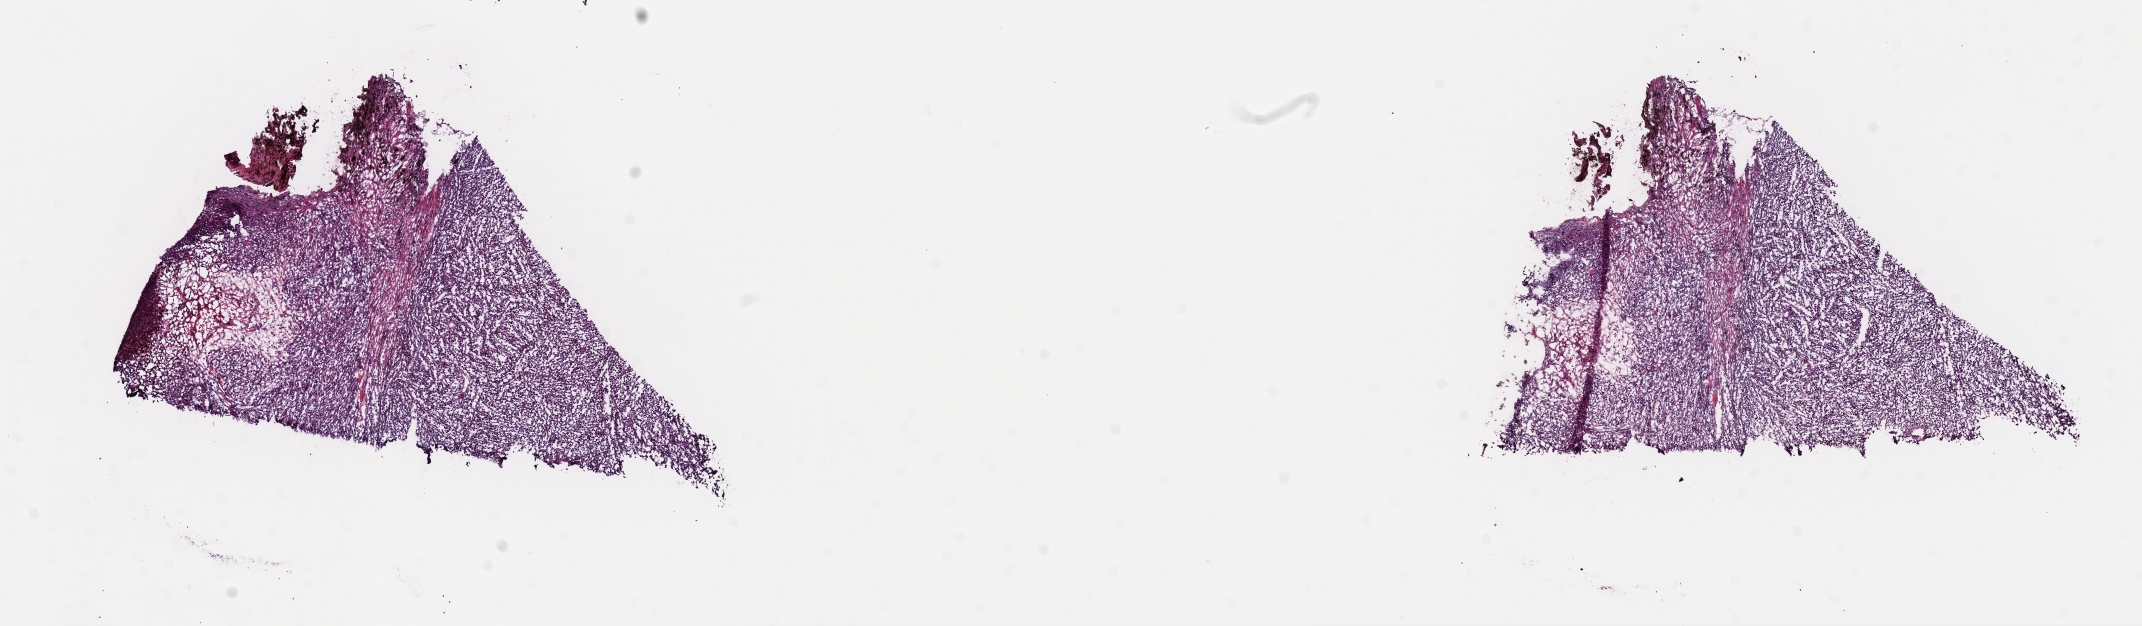
H&E whole-slide image, whole scanned area (about 16.9 x 4.9 mm, acquisition: 40x scan) shown as a low-resolution overview, frozen section from the top of the tissue portion, metastatic tumour sample, sampled site: connective, subcutaneous and other soft tissues of upper limb and shoulder. Male, age 71 years at initial diagnosis. Slide review estimates, as recorded: tumour cells 80%, tumour nuclei 80%, normal cells 0%, stromal cells 15%, necrosis 5%. Inflammatory infiltration, as recorded: lymphocyte infiltration 2%, monocyte infiltration 1%, neutrophil infiltration 0%.
This section: metastatic tumour tissue. Patient diagnosis: Malignant melanoma, NOS.